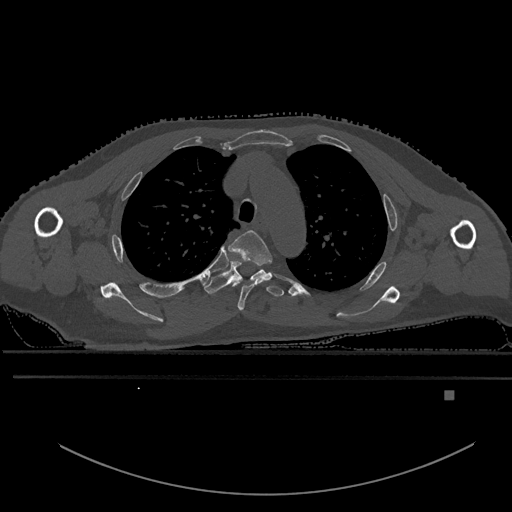
CT including the spine, one axial slice. Slice 428 of 969 in the series (ordered by position). Bone window (W 1800 / L 400 HU). 0.5 mm slice thickness. 512 × 512 image matrix, field of view 456 × 456 mm. Patient: male, 82 years. From the clinical record (not read from this slice): primary cancer: prostate; vertebrae with lytic lesions (as recorded): T11, T9, T8, T2.
Outlined on this slice (semi-automatic segmentation, software-assisted and operator-edited):
- T3 vertebra: box from (x=228, y=230) to (x=273, y=311) px
- T4 vertebra: (x=203, y=261)–(x=284, y=298)